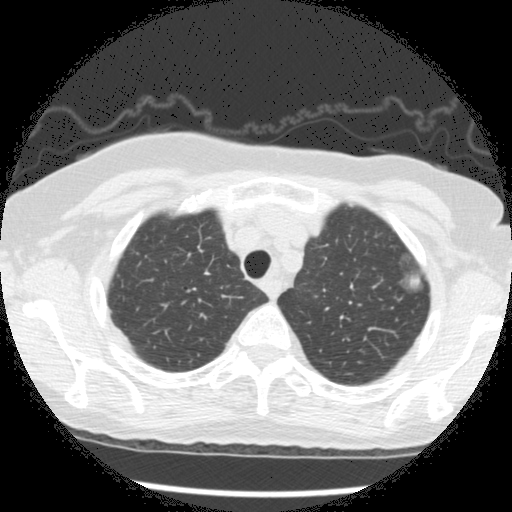
Low-dose screening chest CT, axial slice, second screening round (one year after baseline), lung window (W 1500 / L -600 HU), 2.5 mm slice thickness, 120 kVp, slice 36 of 266 in the series. Female participant, aged 73 years at enrolment.
Expert reader's lesion annotation, bounding box [x1, y1, x2, y2] px = [387, 250, 431, 295]. The screening reader recorded 3 non-calcified nodules or masses ≥4 mm on this exam (left upper lobe, left upper lobe, left upper lobe); which of them this box marks is not recorded. Official screen result: positive, change unspecified: nodule(s) >= 4 mm or enlarging nodule(s), mass(es), or other non-specific abnormalities suspicious for lung cancer. Participant outcome: lung cancer diagnosed 49 days after this screen — bronchiolo-alveolar adenocarcinoma, NOS, left upper lobe, well differentiated (G1), stage IA (AJCC 6th edition), 10 mm at pathology.